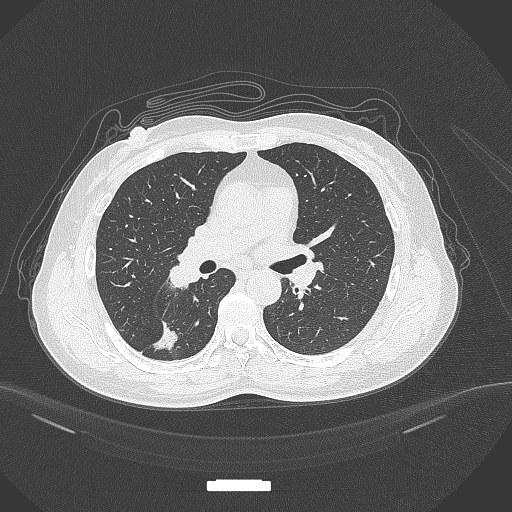
Chest CT, one axial slice. Position 173 of 352 along the scan axis. Lung window (W 1500 / L -600 HU). 1 mm slice thickness. 512 × 512 image matrix, field of view 400 × 400 mm. Patient: female, 55 years. From the clinical record (not read from this slice): clinical TNM (as recorded): T1c N1 M0.
Annotated regions visible in this slice (rectangle marked by the reading radiologist):
- lung tumour (recorded histology: adenocarcinoma): bounding box [x1, y1, x2, y2] px = [146, 314, 187, 353]